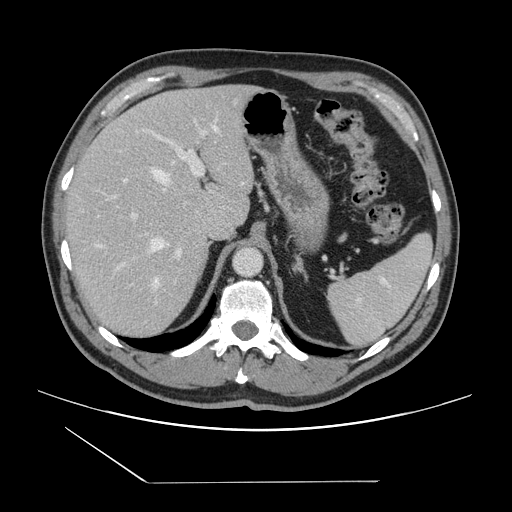
Contrast-enhanced abdominal CT, one axial slice. Slice 102 of 157 in the series (ordered by position). 120 kVp. Intravenous contrast given. Soft-tissue window (W 400 / L 40 HU). 2.5 mm slice thickness. 512 × 512 image matrix, field of view 407 × 407 mm. Male patient, age 61 years. From the clinical record (not read from this slice): diagnosis: colorectal cancer liver metastases, imaged before liver resection; multiple liver metastases: yes; largest metastasis: 5.5 cm.
Annotated regions visible in this slice (manually delineated by an expert):
- hepatic veins: bounding box (x1, y1, x2, y2) in pixels: (151, 125, 218, 287)
- liver: (67, 85, 253, 338)
- planned liver remnant (the part of the liver to remain after resection): (68, 85, 238, 226)
- portal vein (with intrahepatic branches): (97, 130, 206, 268)